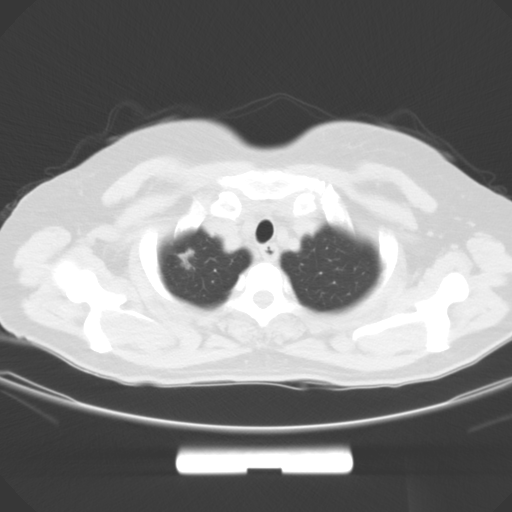
Chest CT, one axial slice; slice 53 of 59 in the series (ordered by position); lung window (W 1500 / L -600 HU); 5 mm slice thickness; 512 × 512 image matrix, field of view 369 × 369 mm. Patient: female, 58 years. From the clinical record (not read from this slice): clinical TNM (as recorded): T1b N0 M0; histopathological grade: G2-3.
Structures marked on this image (rectangle marked by the reading radiologist):
- lung tumour (recorded histology: adenocarcinoma): bounding box (x1, y1, x2, y2) in pixels: (174, 246, 201, 282)